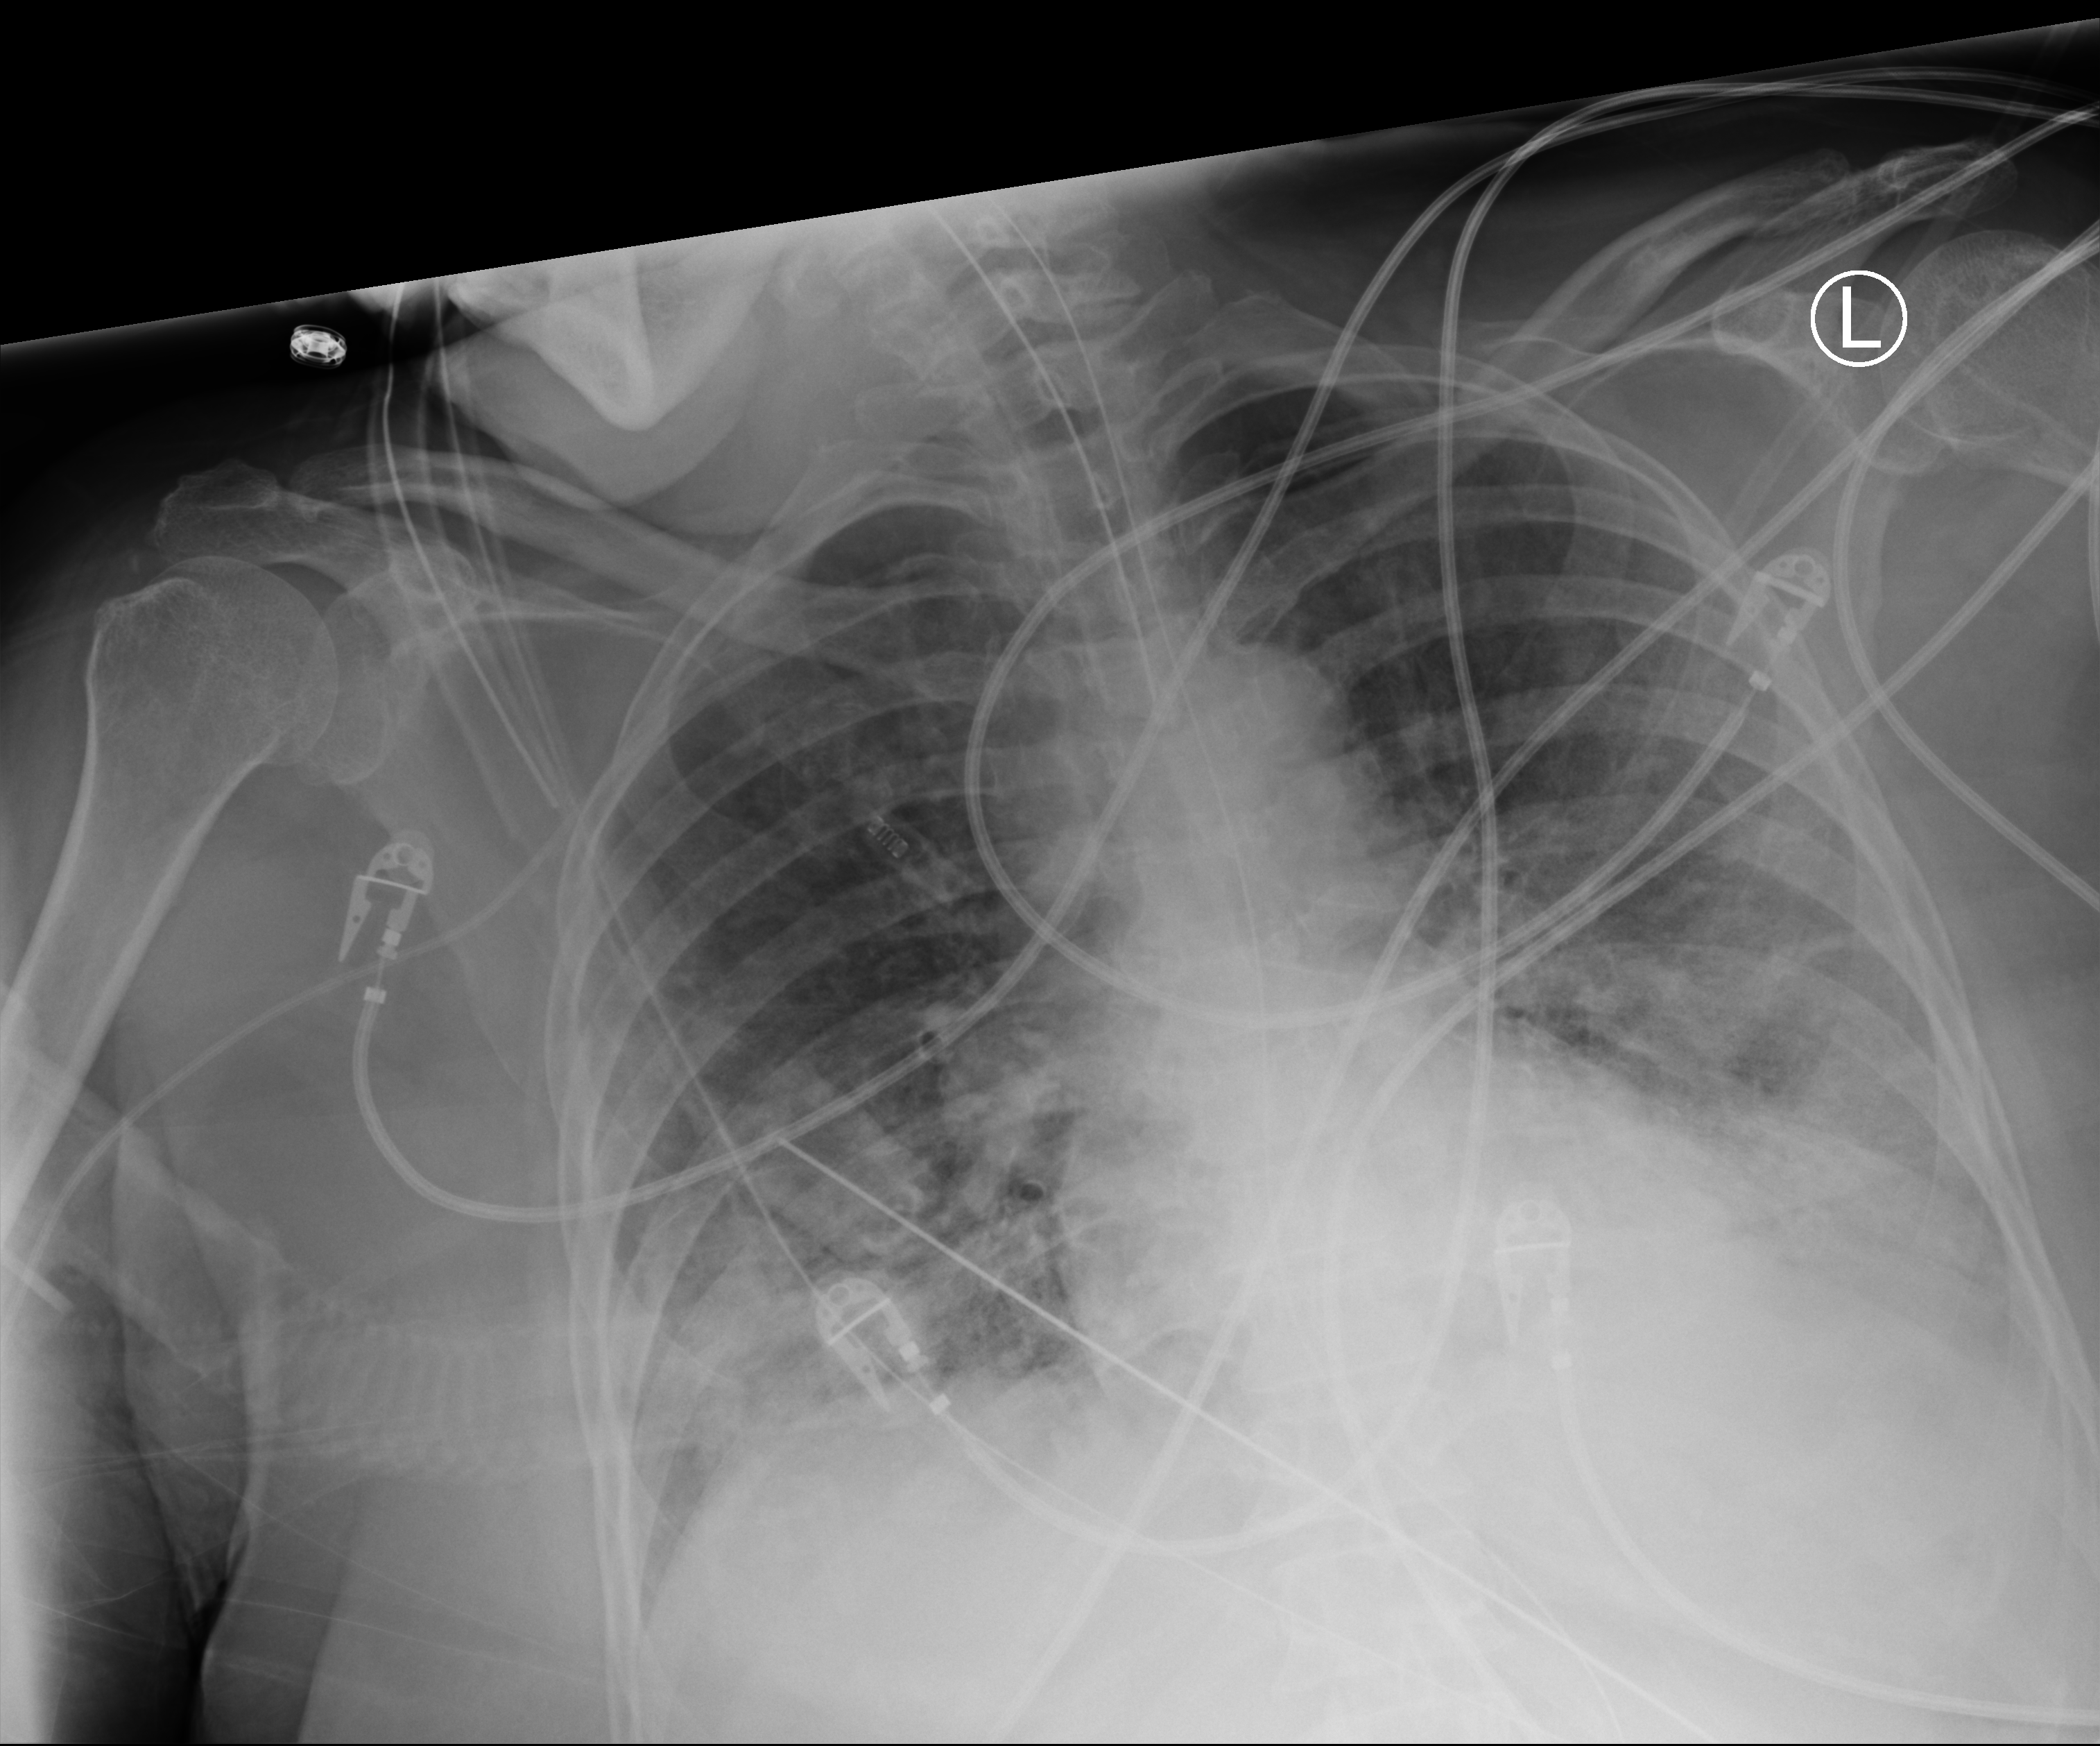
Chest X-ray (portable), anteroposterior (AP) projection. Patient hospitalised with COVID-19; female, aged 75–90 years.
From the hospital-stay record, not from the radiograph (when in the stay this image was taken is not recorded):
- smoking status (admission record): never
- mechanically ventilated during this hospital stay: yes
- hypertension (admission record): yes